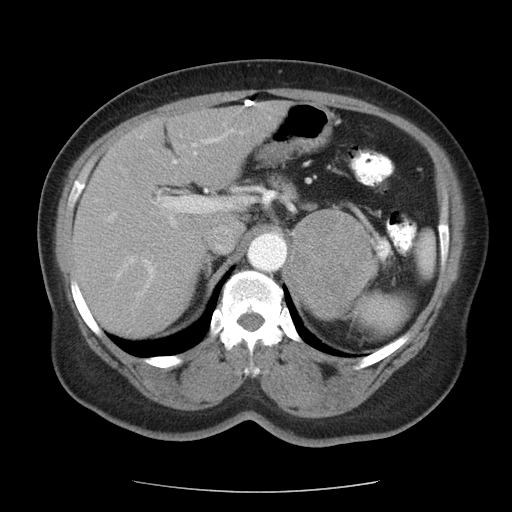
Contrast-enhanced abdominal CT, one axial slice. Reconstruction kernel STANDARD. 120 kVp. Intravenous contrast given. Soft-tissue window (W 400 / L 40 HU). 5 mm slice thickness. 512 × 512 image matrix. Patient: female, 71 years. Case-level facts recorded for this patient, not image findings: diagnosis: adrenocortical carcinoma; tumour side: left adrenal; tumour size at pathology: 8.8 cm; Ki-67 index: 20 %; stage (as recorded): 2.
Outlined on this slice (semi-automatically segmented with operator editing):
- mass: bounding box <288,211,373,316> (left, top, right, bottom; pixels)